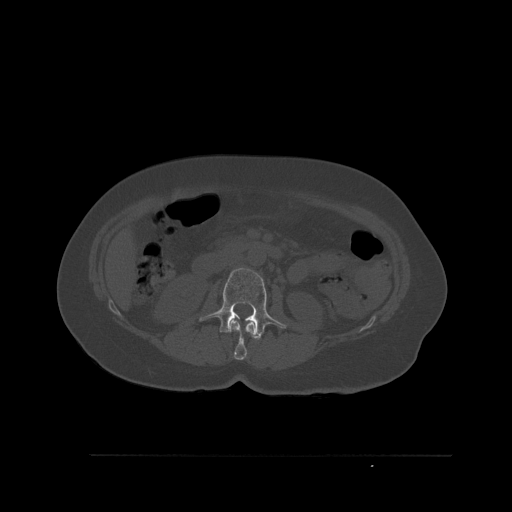
CT including the spine, one axial slice; position 250 of 527 along the scan axis; bone window (W 1800 / L 400 HU); 512 × 512 image matrix, field of view 470 × 470 mm. Female patient, age 73 years. Case-level facts recorded for this patient, not image findings: primary cancer: breast.
Outlined on this slice (semi-automatically segmented with operator editing):
- L1 vertebra: bounding box (x1, y1, x2, y2) in pixels: (229, 319, 261, 360)
- L2 vertebra: (199, 267, 287, 339)